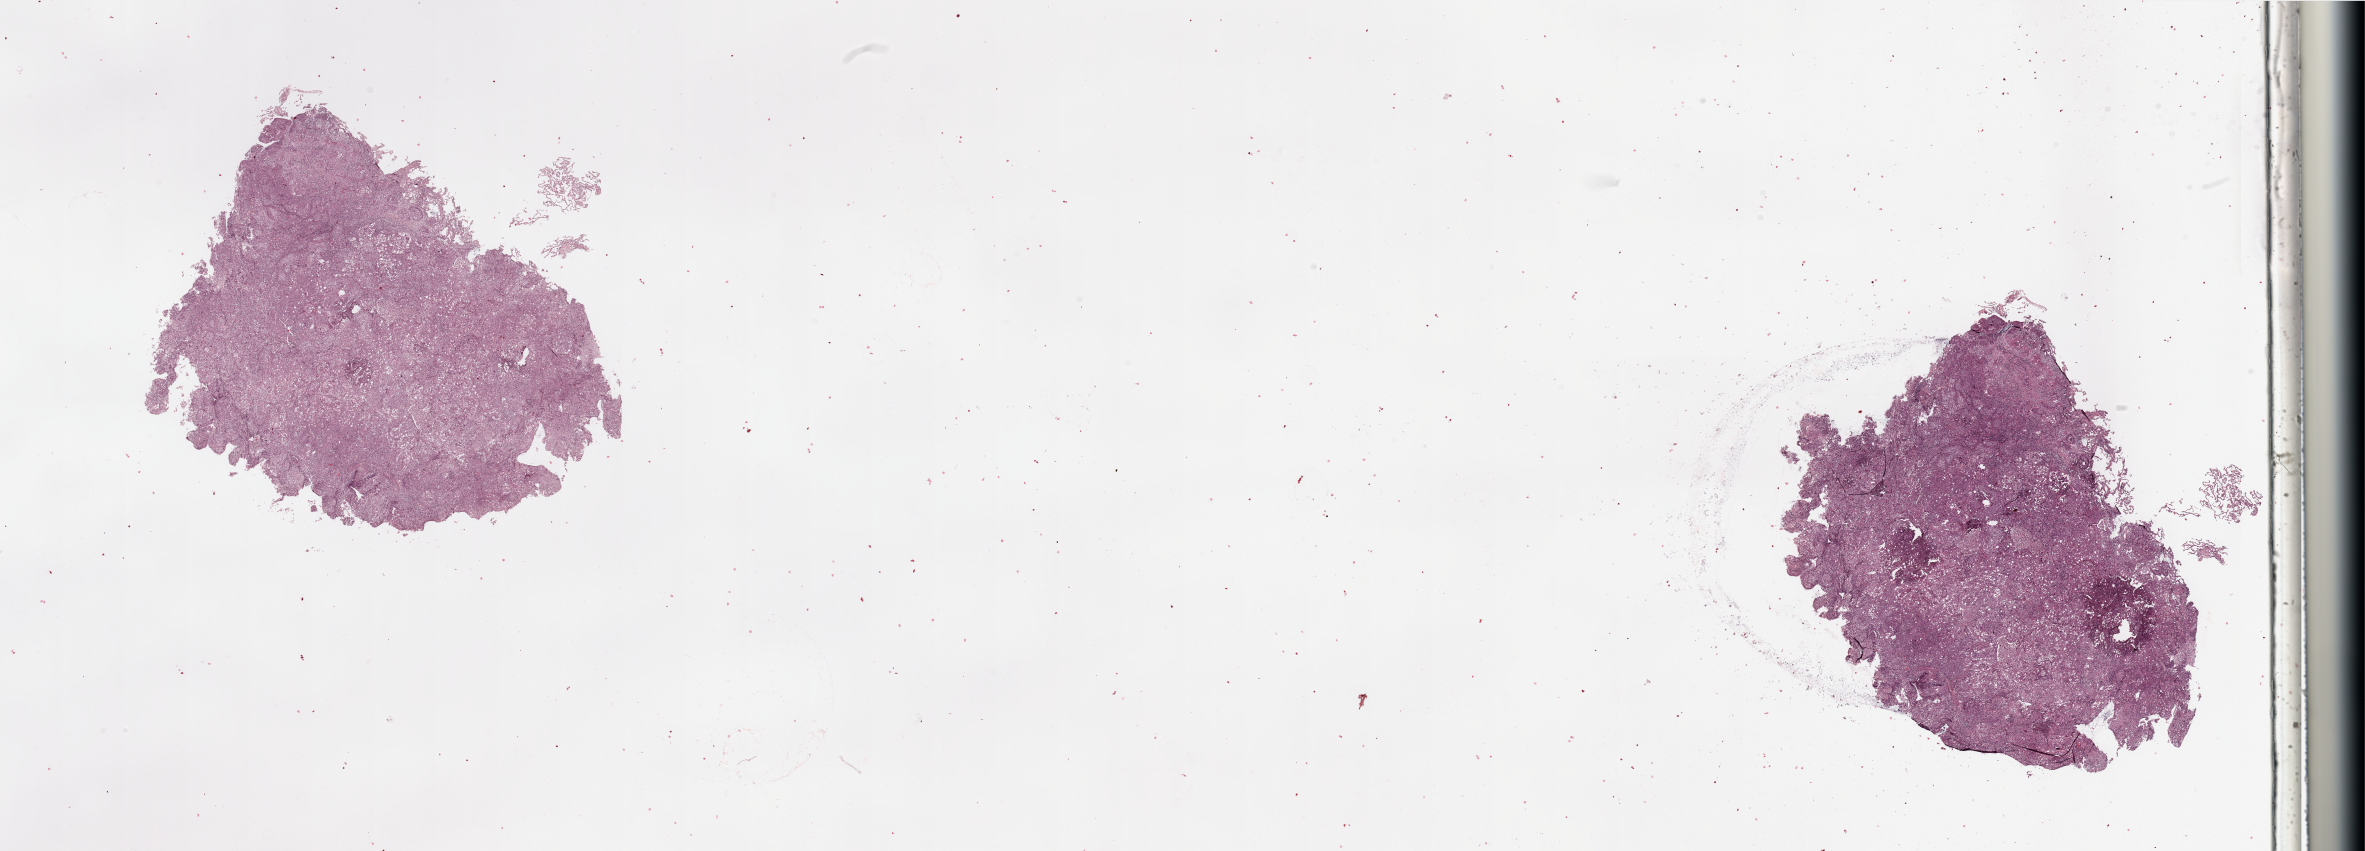
Whole-slide histology image, Hematoxylin and eosin (H&E) stained, low-resolution overview of the scanned area, about 37.4 x 13.5 mm (from a 20x scan). Tumour tissue sample, lung. Patient: male, age 68 years.
Patient diagnosis (cohort enrolment): squamous cell carcinoma (lung).